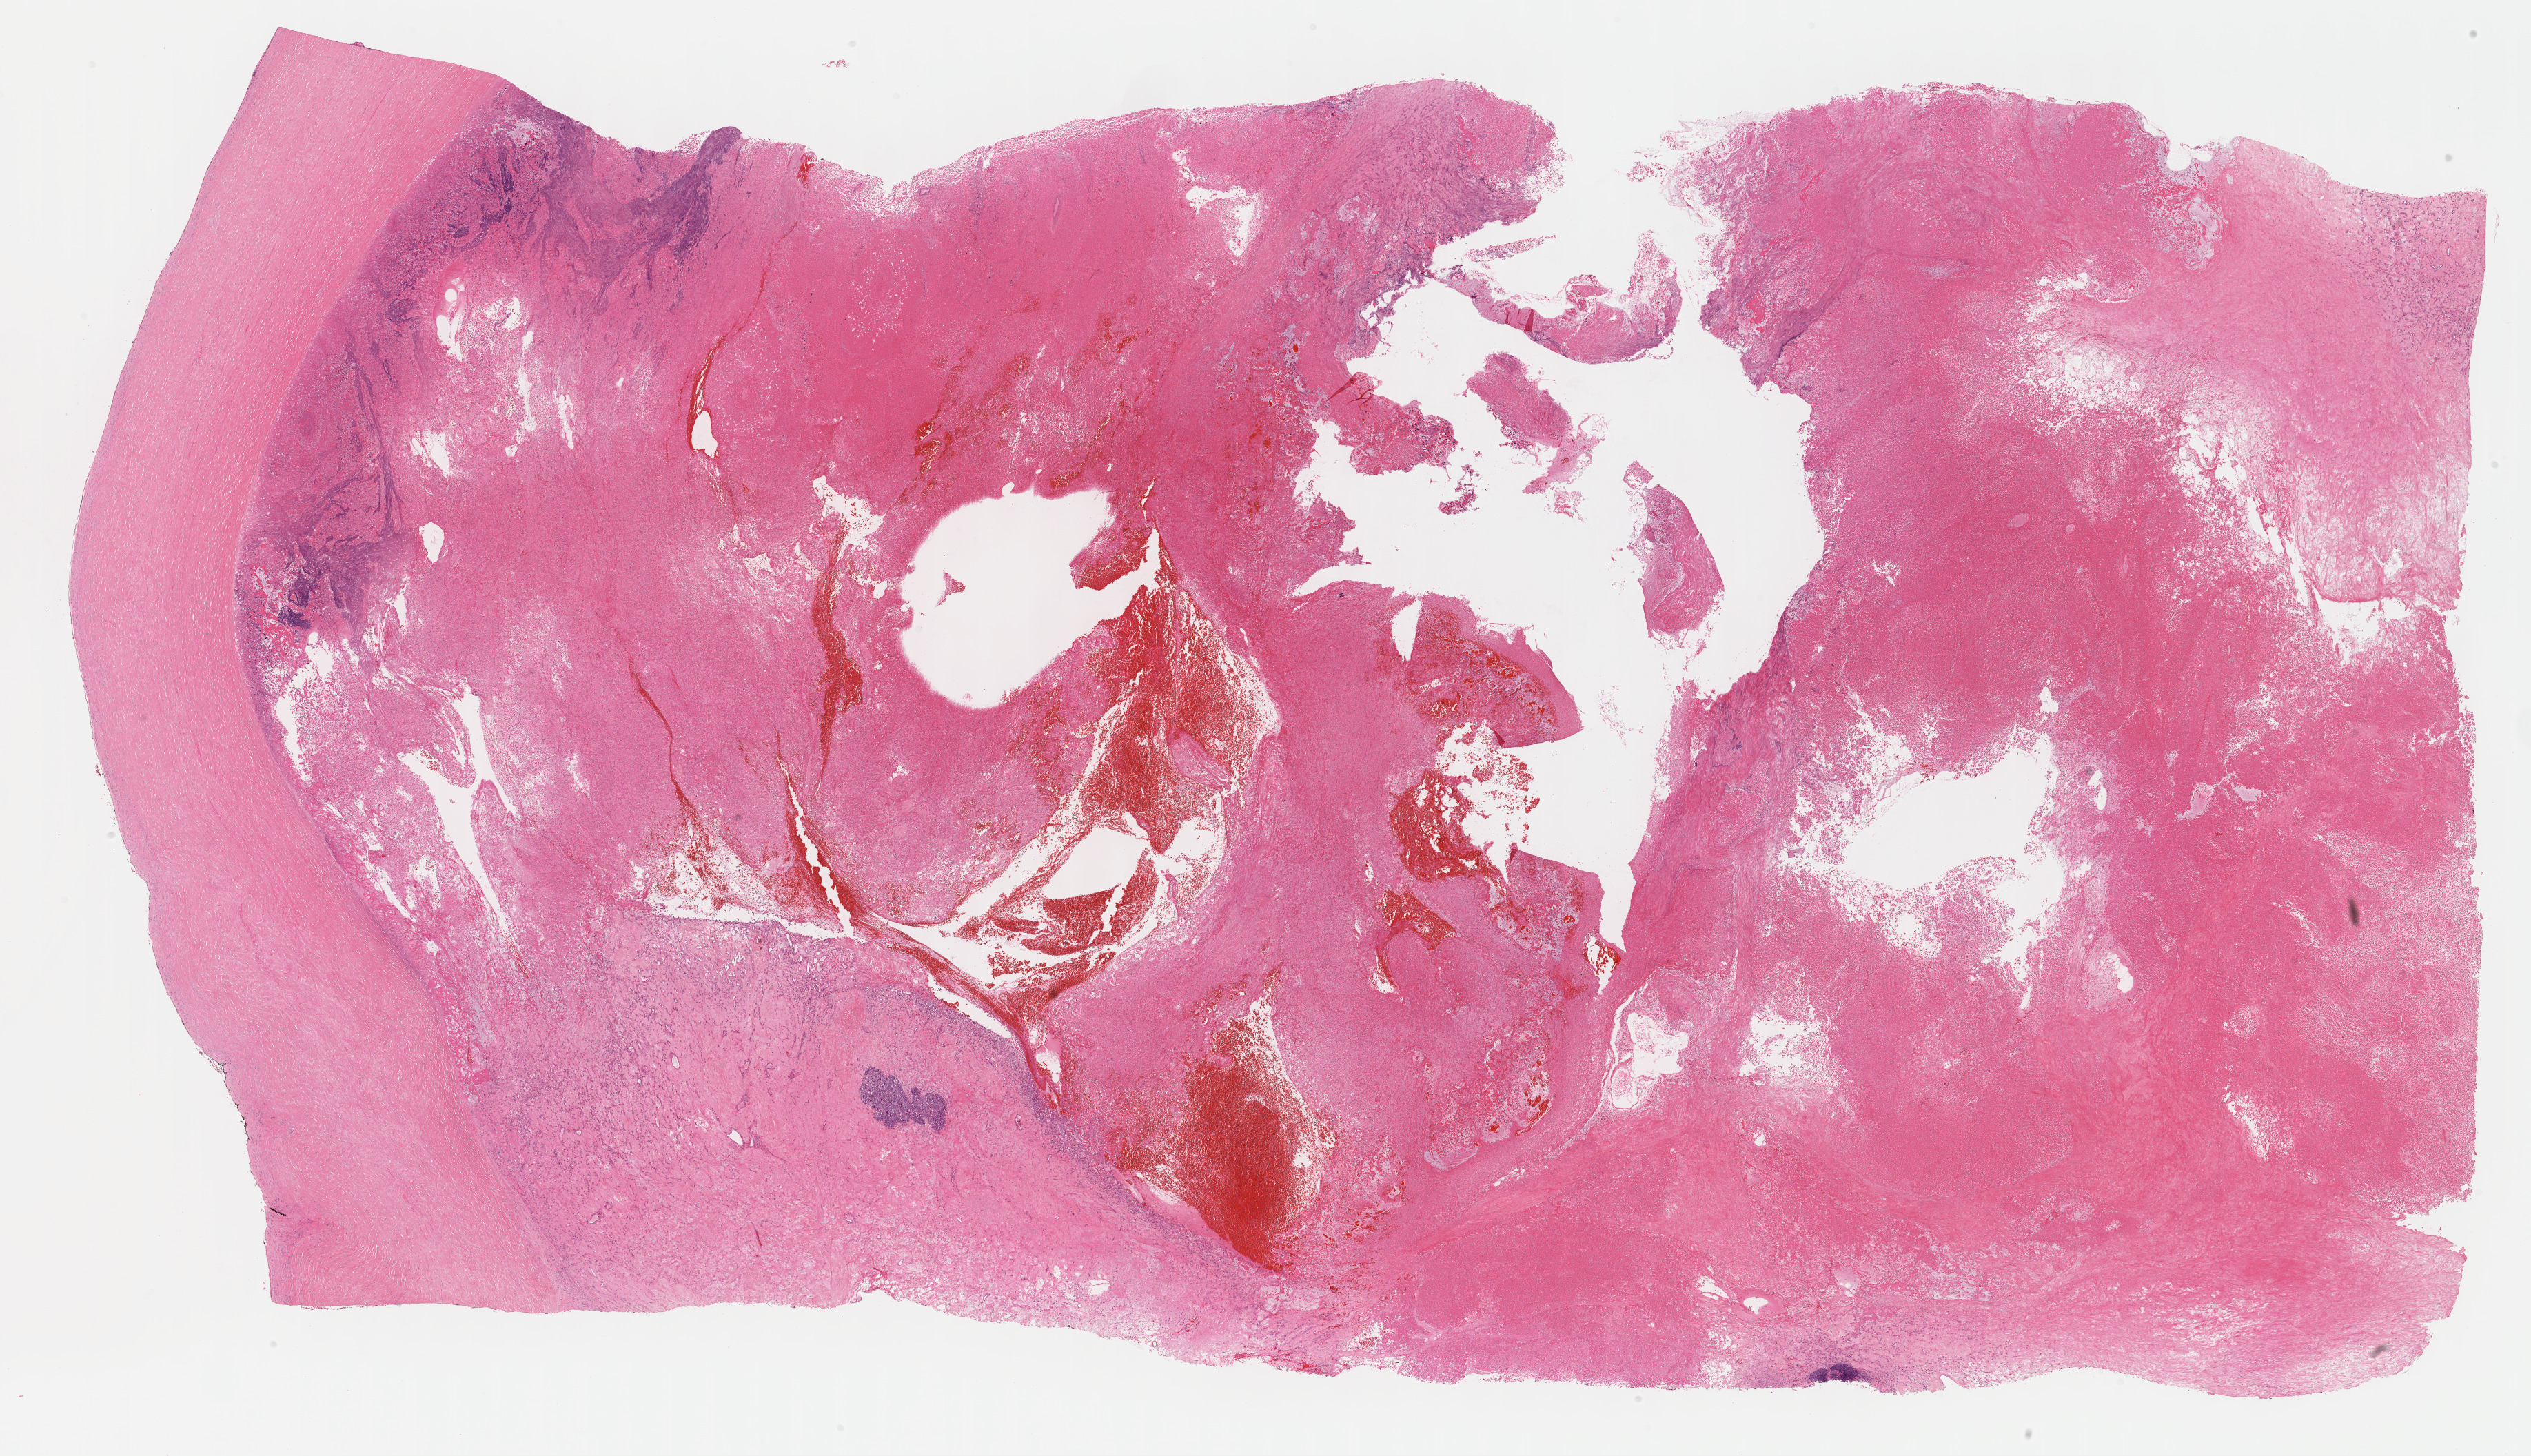
Digitized Hematoxylin and eosin (H&E) stained tissue section (whole slide) — whole scanned area (about 29.7 x 17.1 mm) shown as a low-resolution overview. FFPE section. Primary tumour sample from the ovary. Female, age 51 years at initial diagnosis.
Diagnosis: Serous cystadenocarcinoma, NOS.